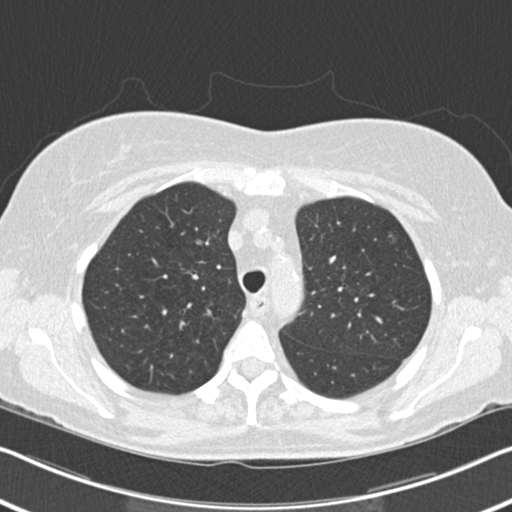
Low-dose screening chest CT, axial slice; second screening round (one year after baseline); lung window (W 1500 / L -600 HU); 2 mm slice thickness; slice 54 of 202 in the series. Female participant, aged 60 years at enrolment. Current smoker at enrolment.
Lesion marked by an expert reader, bounding box <374,224,413,264> (left, top, right, bottom; pixels). The screening reader recorded 6 non-calcified nodules or masses ≥4 mm on this exam (right upper lobe, right middle lobe, right lower lobe, right lower lobe, left lower lobe, lingula); which of them this box marks is not recorded. Official screen result: positive, change unspecified: nodule(s) >= 4 mm or enlarging nodule(s), mass(es), or other non-specific abnormalities suspicious for lung cancer. Lung cancer was diagnosed 495 days after this screen: non-small cell carcinoma, left upper lobe, poorly differentiated (G3), stage IB (AJCC 6th edition), 7 mm at pathology.